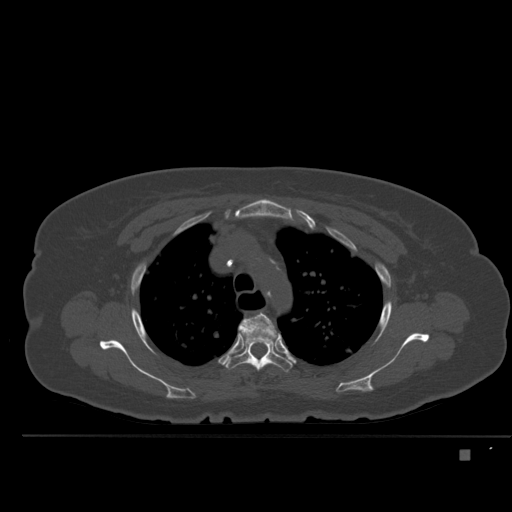
CT including the spine, one axial slice; position 371 of 477 along the scan axis; bone window (W 1800 / L 400 HU); 512 × 512 image matrix. Female patient, age 74 years. From the clinical record (not read from this slice): primary cancer: colon.
Outlined on this slice (semi-automatic segmentation, software-assisted and operator-edited):
- T3 vertebra: box from (x=238, y=312) to (x=279, y=344) px
- T4 vertebra: (x=225, y=327)–(x=292, y=372)